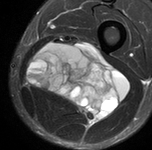
MRI of an extremity soft-tissue mass, one axial slice. Position 41 of 90 along the scan axis. STIR. MR volume resampled by the dataset authors to the PET/CT grid (not the native acquisition matrix). 3.27 mm slice thickness. 152 × 150 image matrix, field of view 148 × 146 mm. Male patient. From the clinical record (not read from this slice): histological type: undifferentiated pleomorphic liposarcoma; grade: high; site of the primary tumour: left thigh.
Annotated regions visible in this slice (expert contour drawn on MRI and transferred to this co-registered scan by the dataset authors):
- gross tumour volume including surrounding oedema: bounding box [x1, y1, x2, y2] px = [27, 41, 129, 124]
- gross tumour volume (mass): [27, 43, 129, 124]